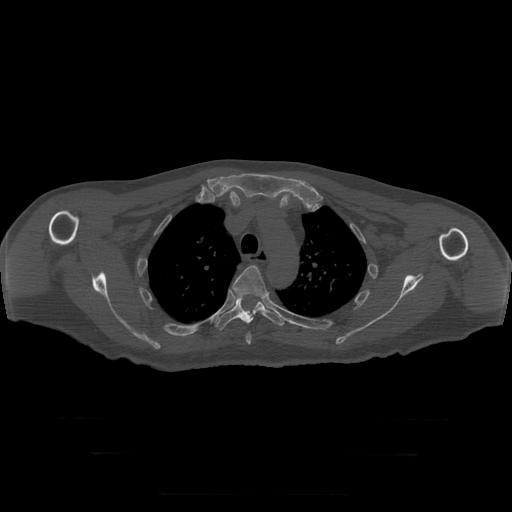
CT including the spine, one axial slice. Slice 234 of 397 in the series (ordered by position). Reconstruction kernel STANDARD. Bone window (W 1800 / L 400 HU). 1.25 mm slice thickness. 512 × 512 image matrix. Patient age 73 years. Case-level facts recorded for this patient, not image findings: primary cancer: prostate.
Annotated regions visible in this slice (semi-automatic segmentation, software-assisted and operator-edited):
- T4 vertebra: bounding box (x1, y1, x2, y2) in pixels: (232, 266, 267, 345)
- T5 vertebra: (216, 297, 285, 330)